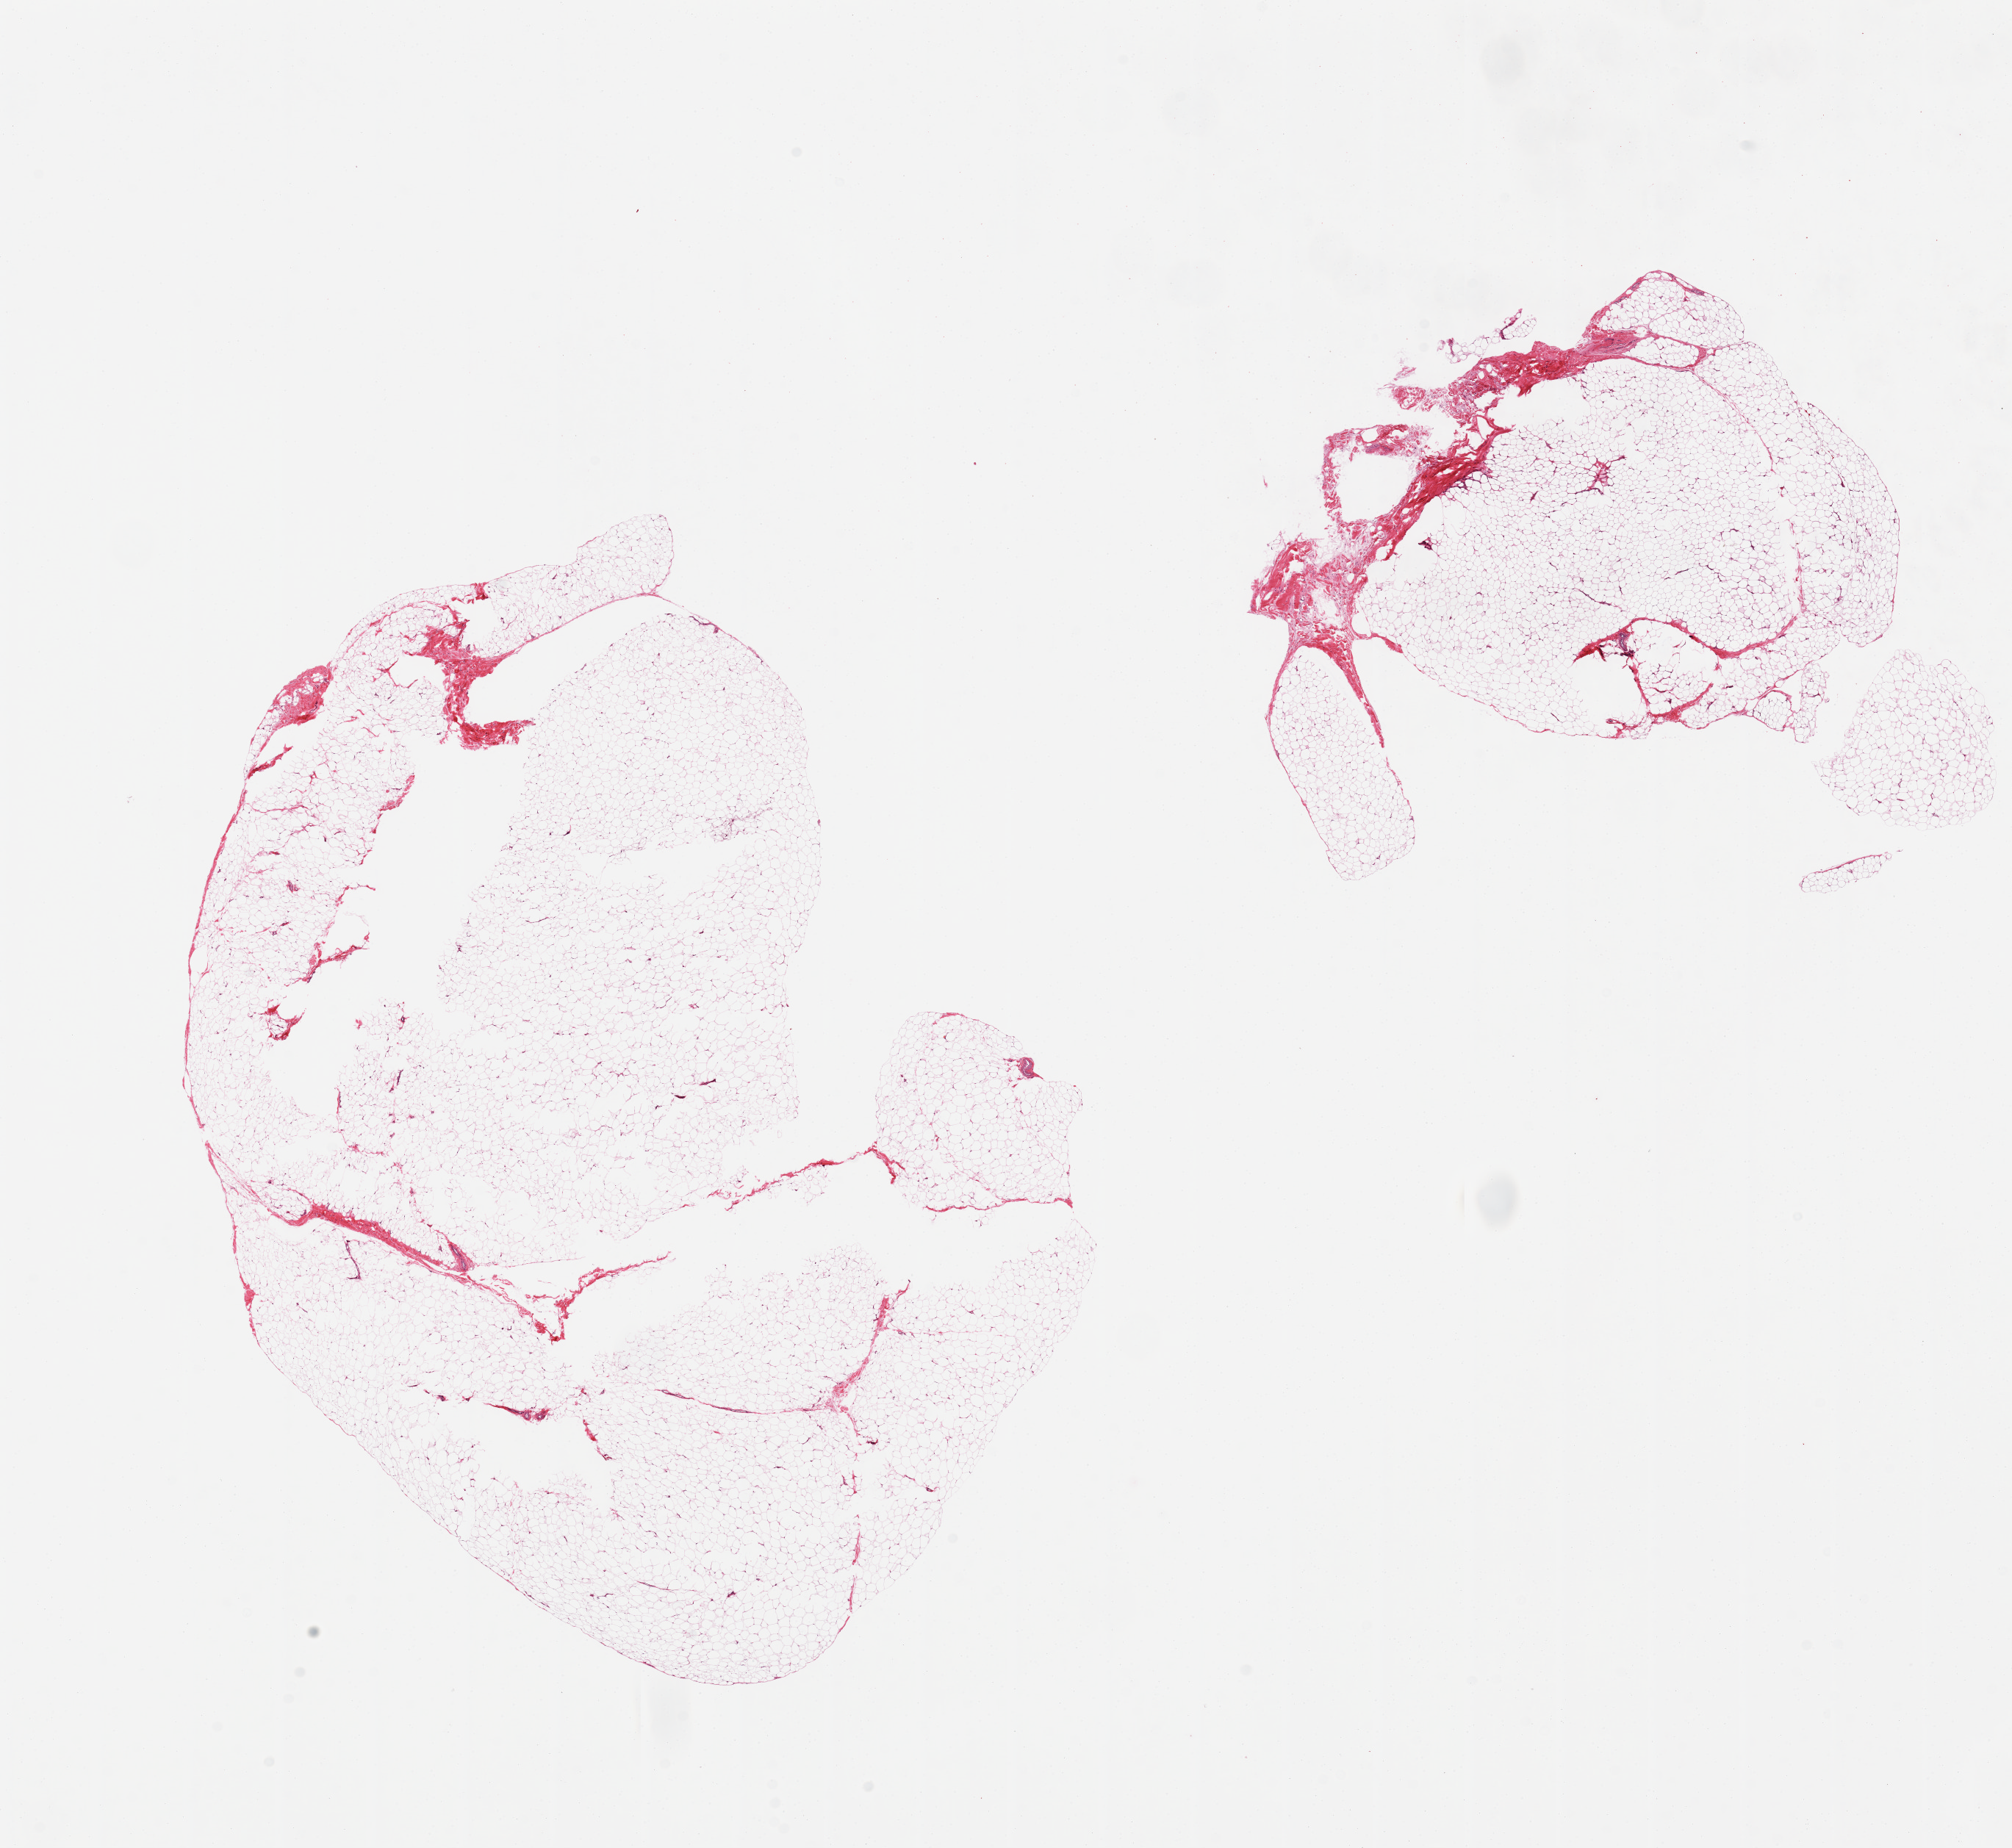
Hematoxylin and eosin (H&E) whole-slide image, a low-resolution overview of the entire scanned area, about 21.7 x 19.9 mm (from a 20x scan), PAXgene-fixed paraffin-embedded (PFPE) section, target tissue: adipose tissue, donor tissue sample.
Pathologist's review note for this sample: 2 pieces; scattered tissue holes.